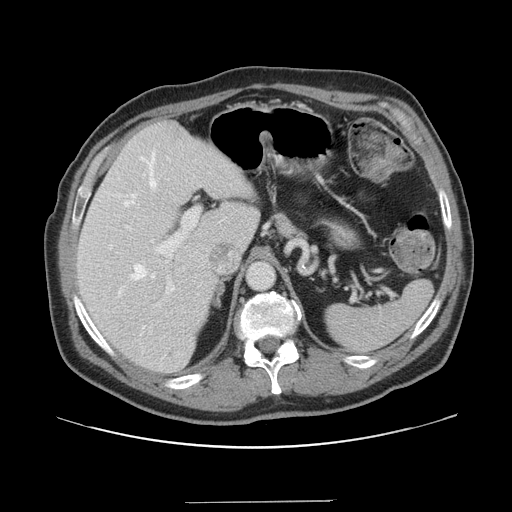
Contrast-enhanced abdominal CT, one axial slice. Position 102 of 151 along the scan axis. 120 kVp. Intravenous contrast given. Soft-tissue window (W 400 / L 40 HU). 2.5 mm slice thickness. 512 × 512 image matrix, field of view 399 × 399 mm. Male patient, age 63 years. Case-level facts recorded for this patient, not image findings: diagnosis: colorectal cancer liver metastases, imaged before liver resection; multiple liver metastases: no; largest metastasis: 2.1 cm; chemotherapy before resection: no.
Outlined on this slice (expert manual segmentation):
- hepatic veins: bounding box [x1, y1, x2, y2] px = [119, 151, 157, 329]
- liver: [78, 121, 260, 373]
- planned liver remnant (the part of the liver to remain after resection): [78, 121, 259, 373]
- portal vein (with intrahepatic branches): [155, 208, 200, 306]